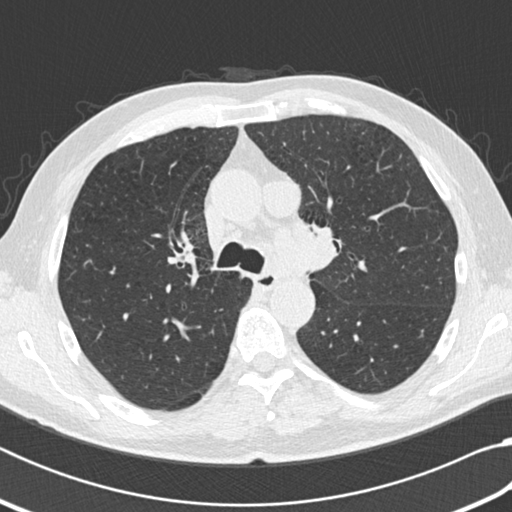
Chest CT (low-dose screening protocol), one axial image. Third screening round (two years after baseline). Lung window (W 1500 / L -600 HU). 2 mm slice thickness. Slice 69 of 207 in the series. Male participant, aged 64 years at enrolment. Current smoker at enrolment.
Expert reader's lesion annotation, bounding box (x1, y1, x2, y2) in pixels: (252, 176, 296, 217). No non-calcified nodule or mass ≥4 mm was recorded by the screening reader at this exam. Official screen result: negative screen, significant abnormalities not suspicious for lung cancer.